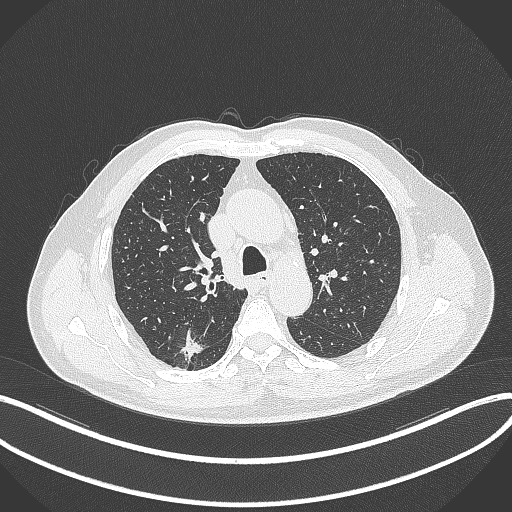
Chest CT, one axial slice; position 258 of 359 along the scan axis; reconstruction kernel B70f; 120 kVp; lung window (W 1500 / L -600 HU); 1 mm slice thickness; 512 × 512 image matrix, field of view 400 × 400 mm. Patient: male, 69 years. Case-level facts recorded for this patient, not image findings: clinical TNM (as recorded): T1b N0 M0; histopathological grade: G2-3.
Structures marked on this image (bounding box drawn by a radiologist):
- lung tumour (recorded histology: adenocarcinoma): bounding box (x1, y1, x2, y2) in pixels: (174, 328, 206, 364)